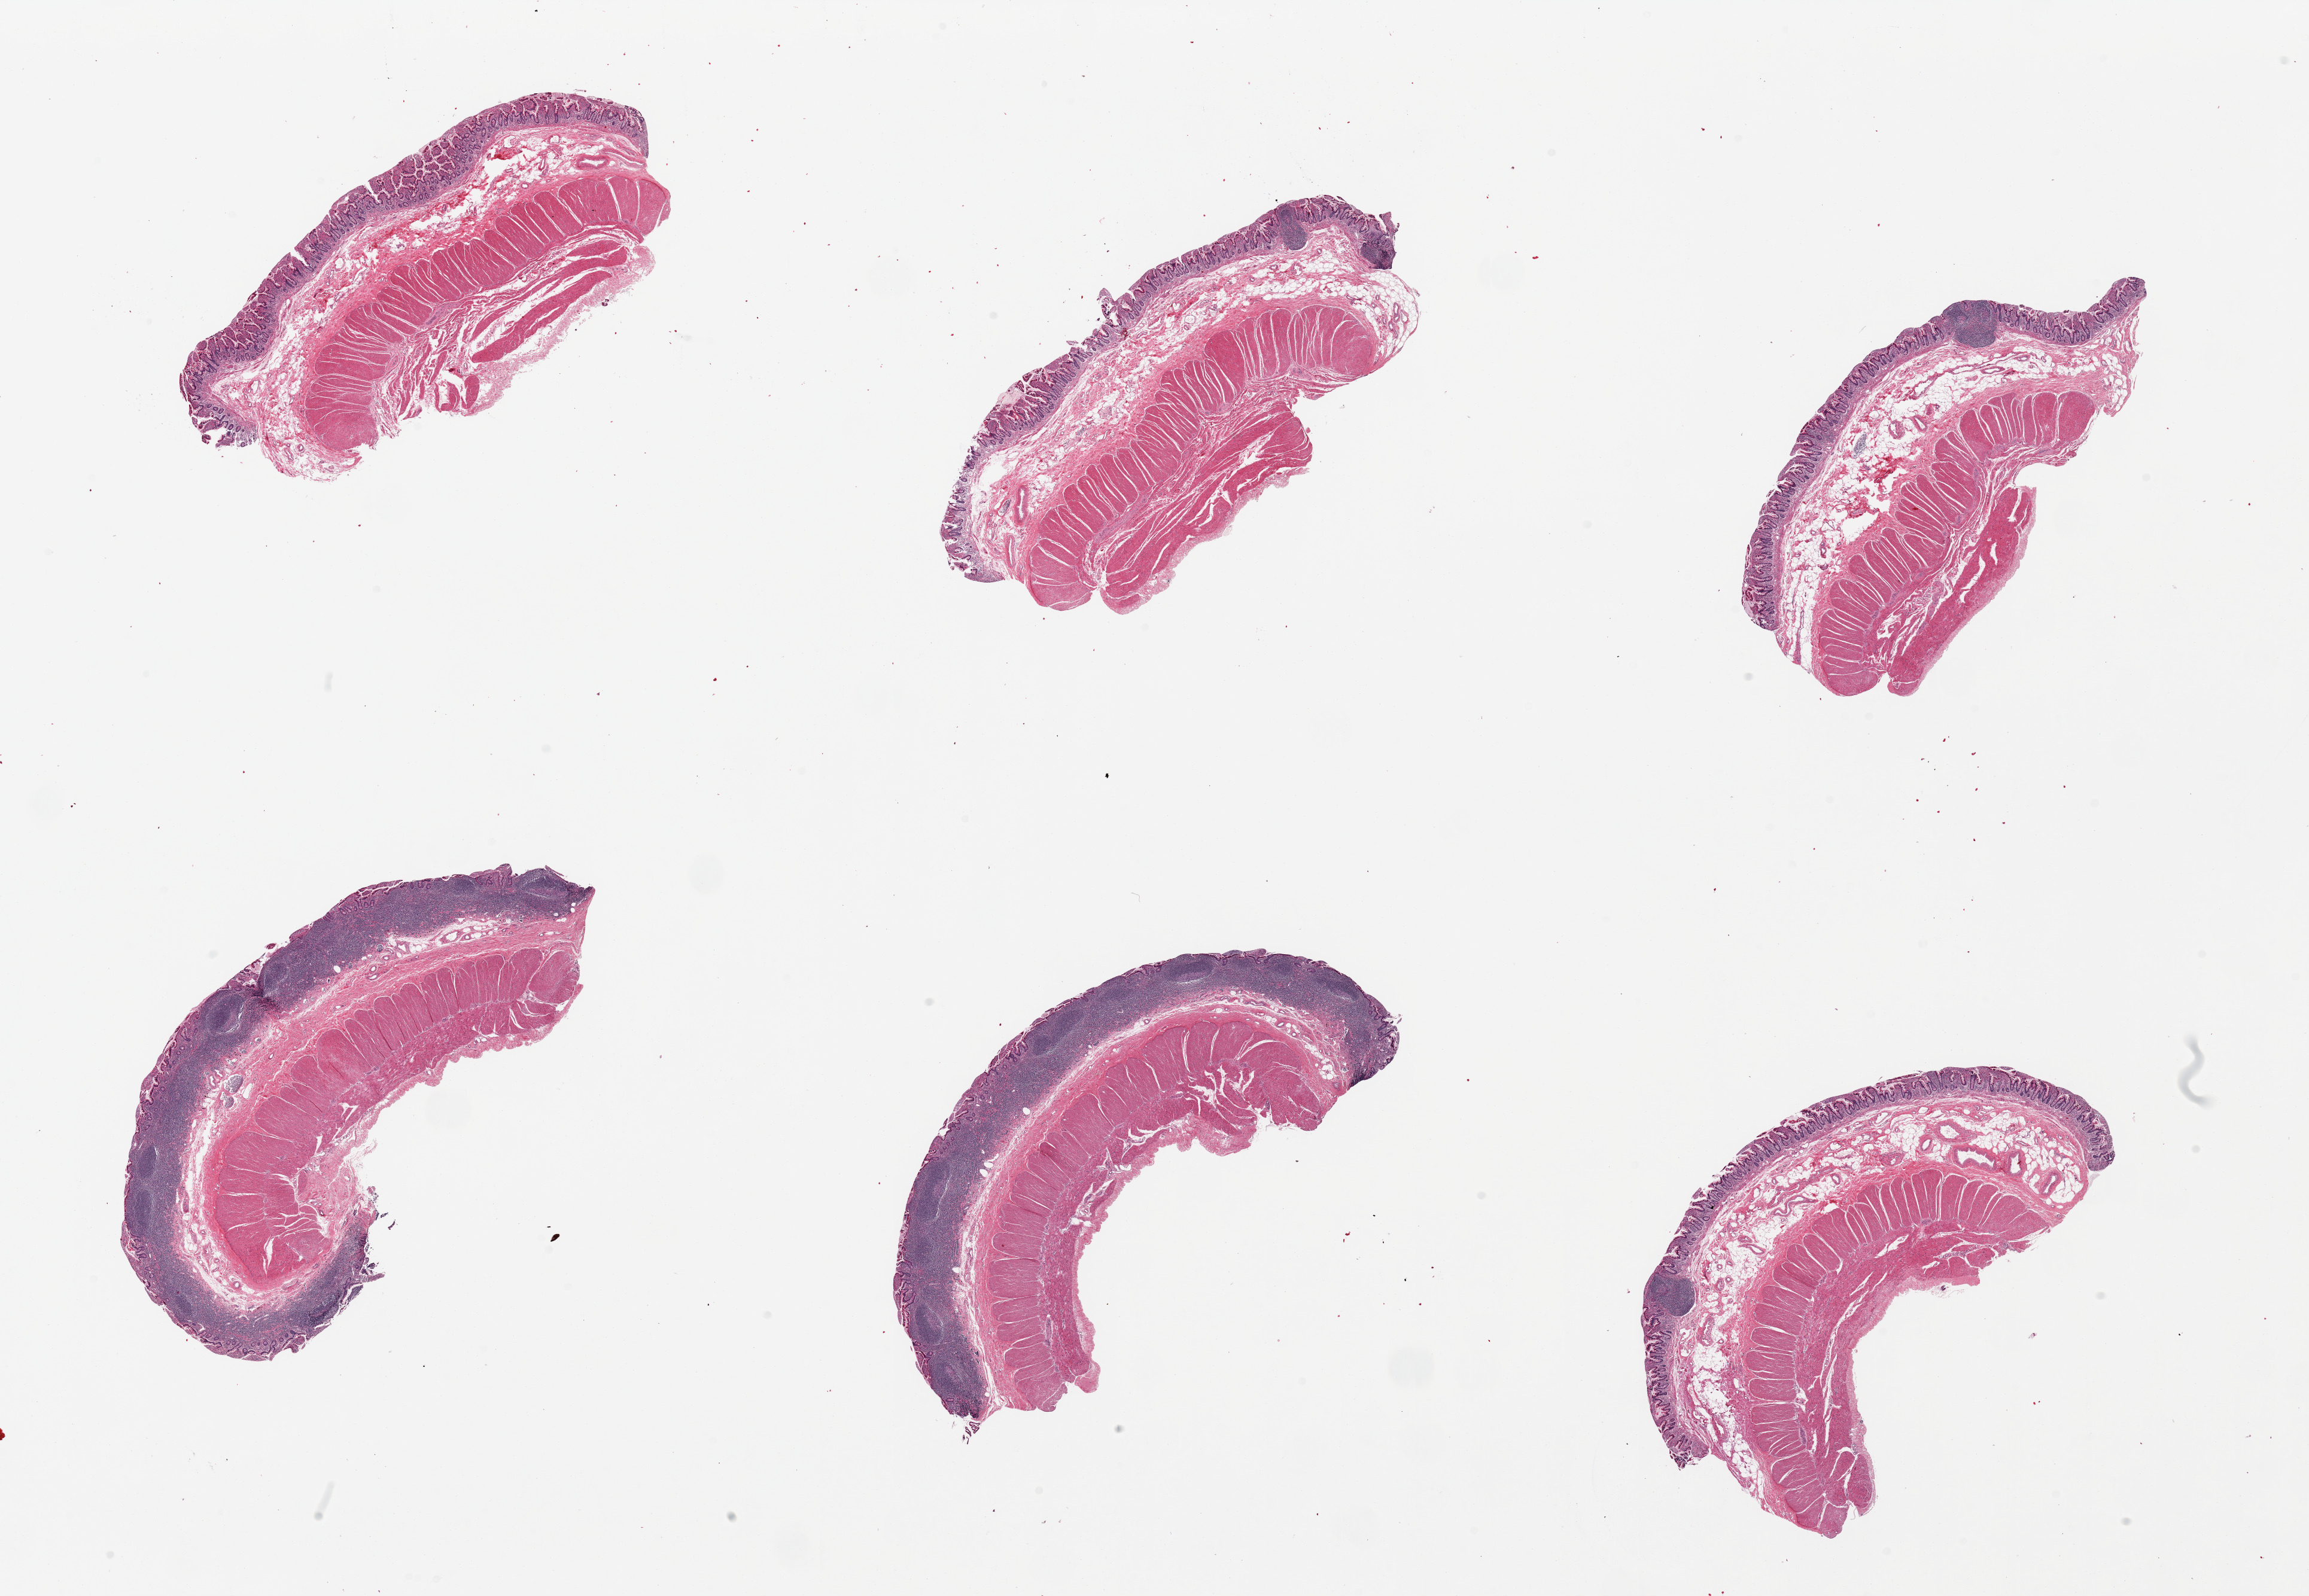
Whole-slide image, hematoxylin and eosin (H&E) stain, shown as a low-resolution overview of the whole scanned area (about 30.5 x 21.1 mm, acquisition: 20x scan). PAXgene-fixed paraffin-embedded (PFPE) section. Target tissue: ileum. Tissue donor sample. Donor: male.
Pathologist's review note for this sample: 6 pieces, two with abundant mucosal lymphoid tissue , other with ileocecal mucosa with focal lymphoid aggregates, all also have abundant muscularis (not target).